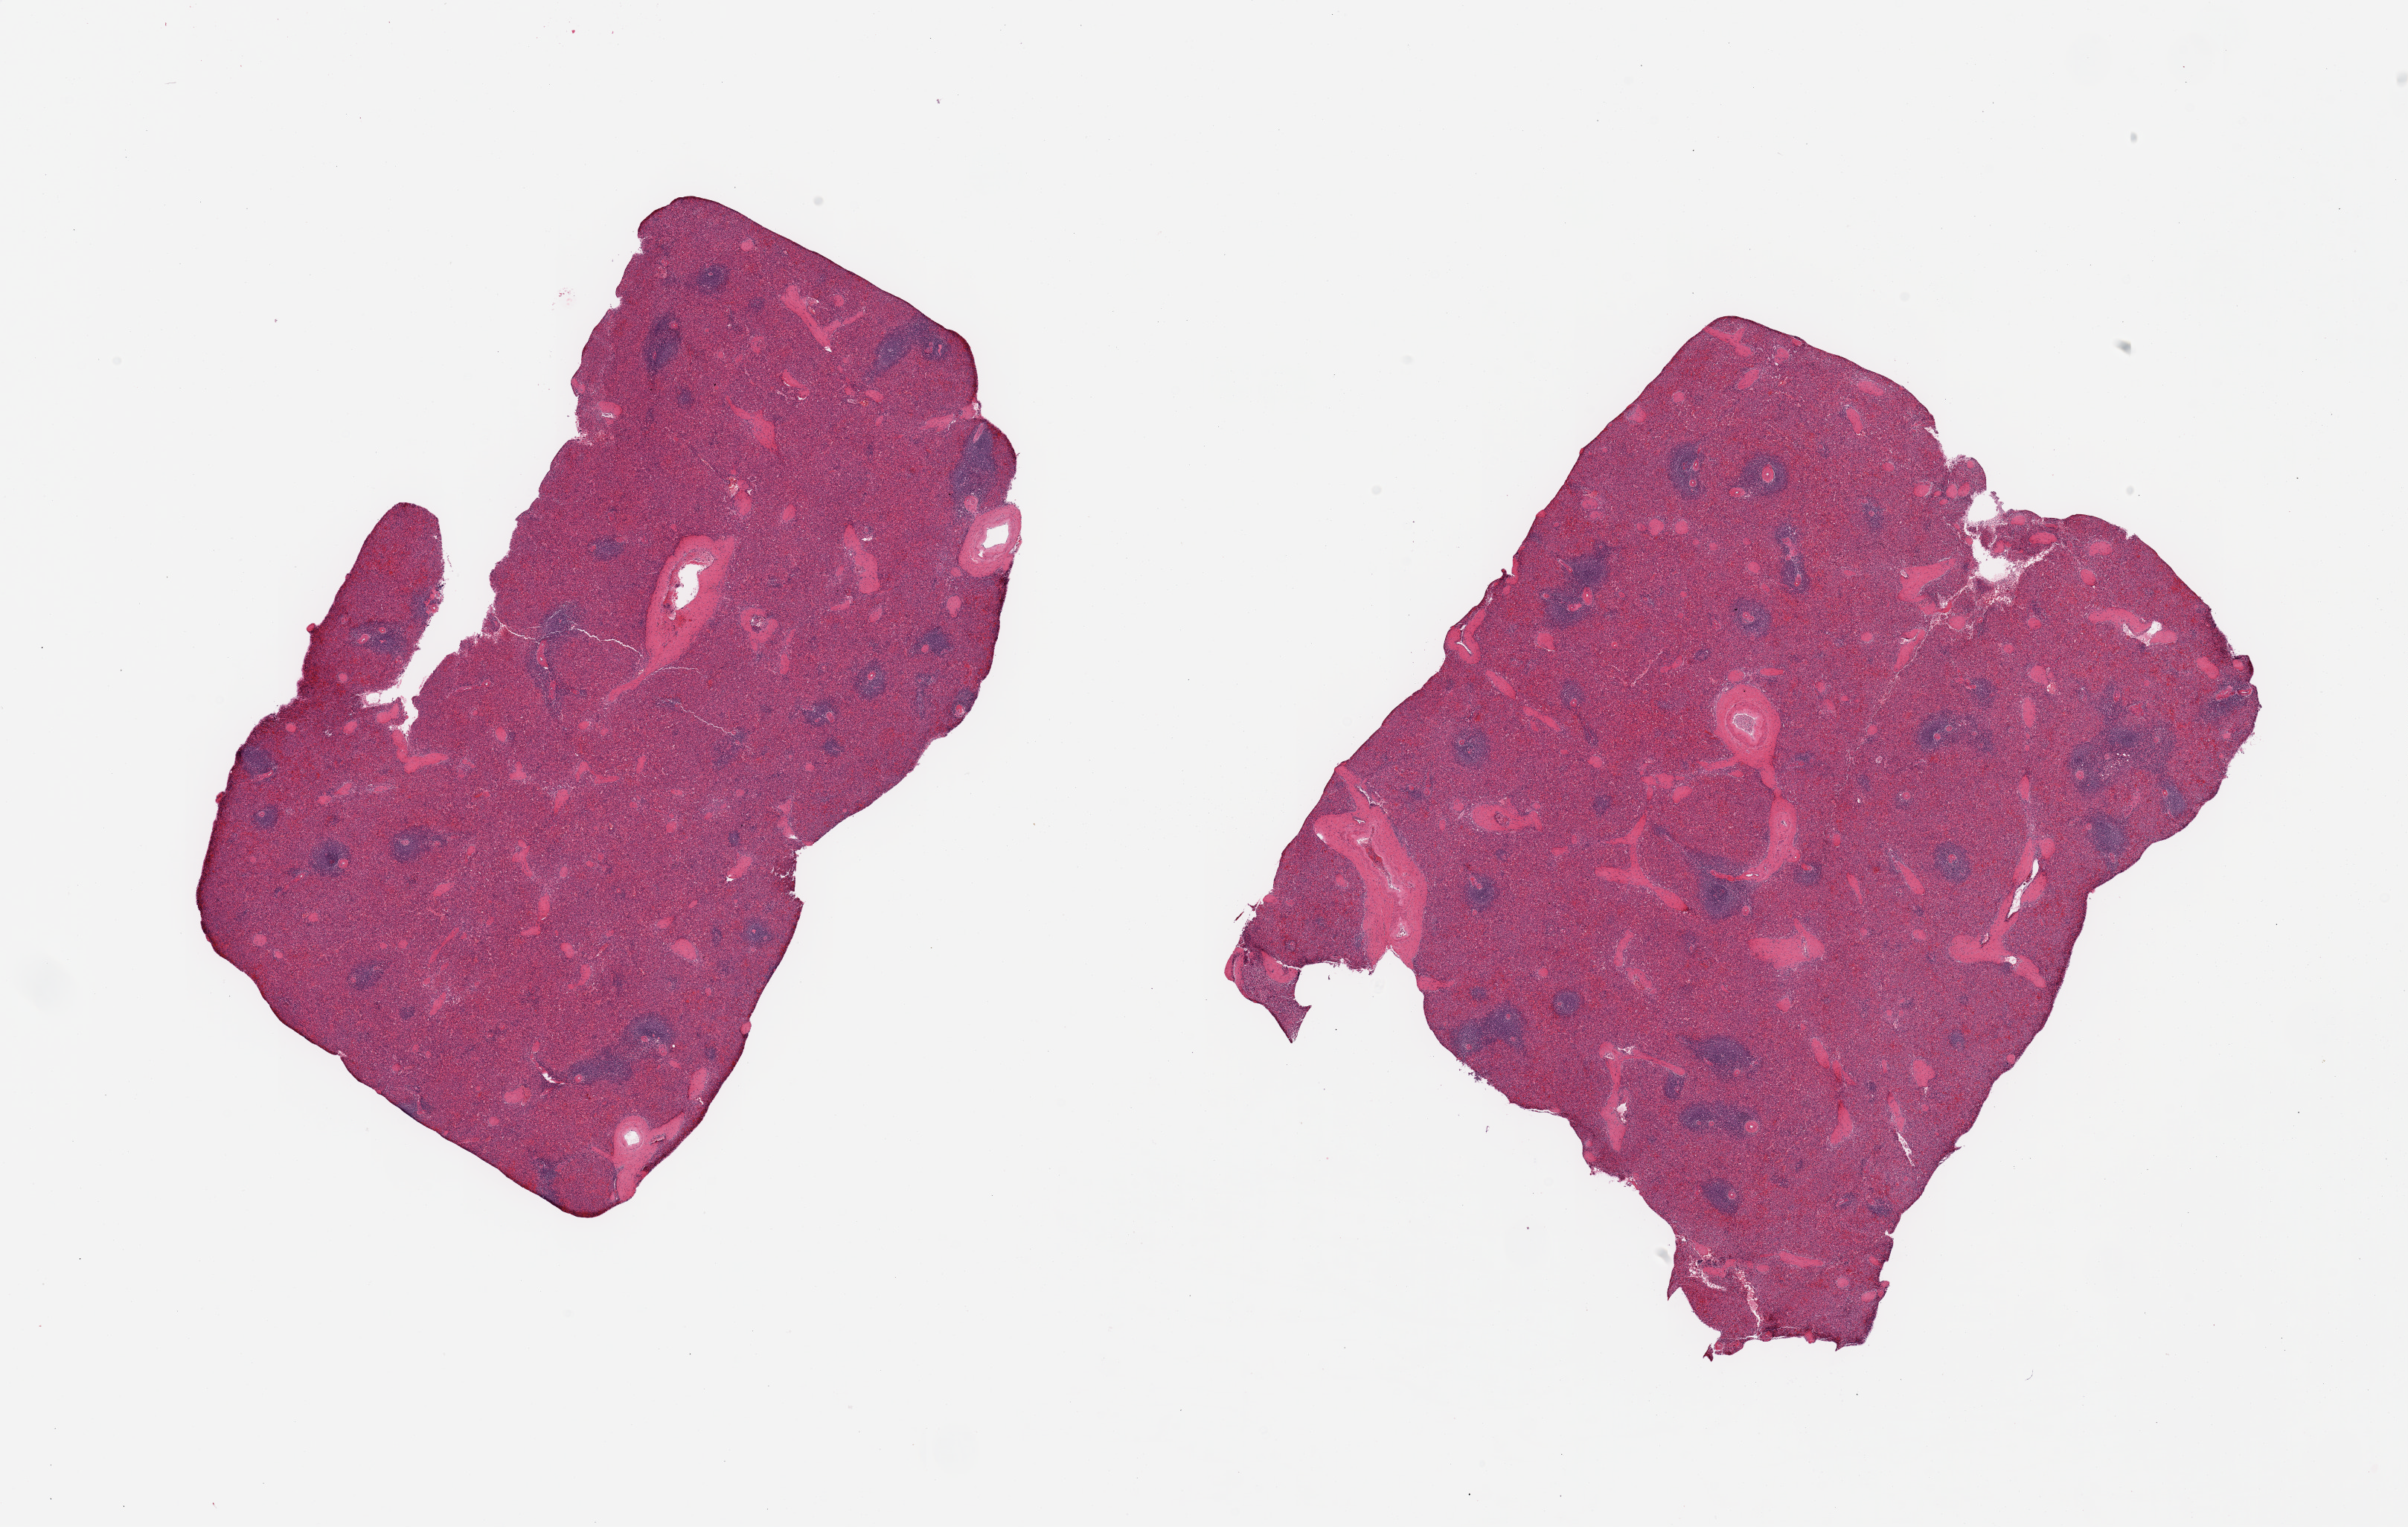
Digitized haematoxylin and eosin-stained section — low-resolution overview of the scanned area, about 25.6 x 16.2 mm (slide scanned at 20x). PAXgene-fixed paraffin-embedded (PFPE) section. Sampled site (target tissue): spleen. Donor tissue sample.
Pathologist's review note for this sample: 2 pieces, no abnormalities.